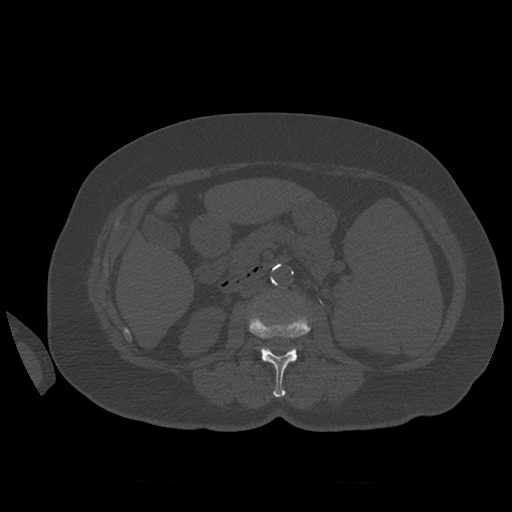
CT including the spine, one axial slice. Reconstruction kernel STANDARD. 120 kVp. Bone window (W 1800 / L 400 HU). 1.25 mm slice thickness. 512 × 512 image matrix. Patient age 81 years. From the clinical record (not read from this slice): primary cancer: renal.
Annotated regions visible in this slice (semi-automatically segmented with operator editing):
- L2 vertebra: bounding box [x1, y1, x2, y2] px = [249, 312, 311, 398]